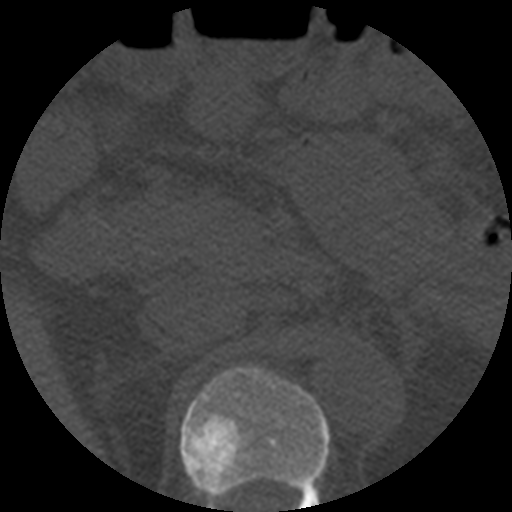
CT including the spine, one axial slice. Bone window (W 1800 / L 400 HU). 1.25 mm slice thickness. 512 × 512 image matrix, field of view 160 × 160 mm. Patient age 57 years. Case-level facts recorded for this patient, not image findings: primary cancer: prostate.
Outlined on this slice (semi-automatic segmentation, software-assisted and operator-edited):
- T12 vertebra: box from (x=180, y=365) to (x=330, y=512) px